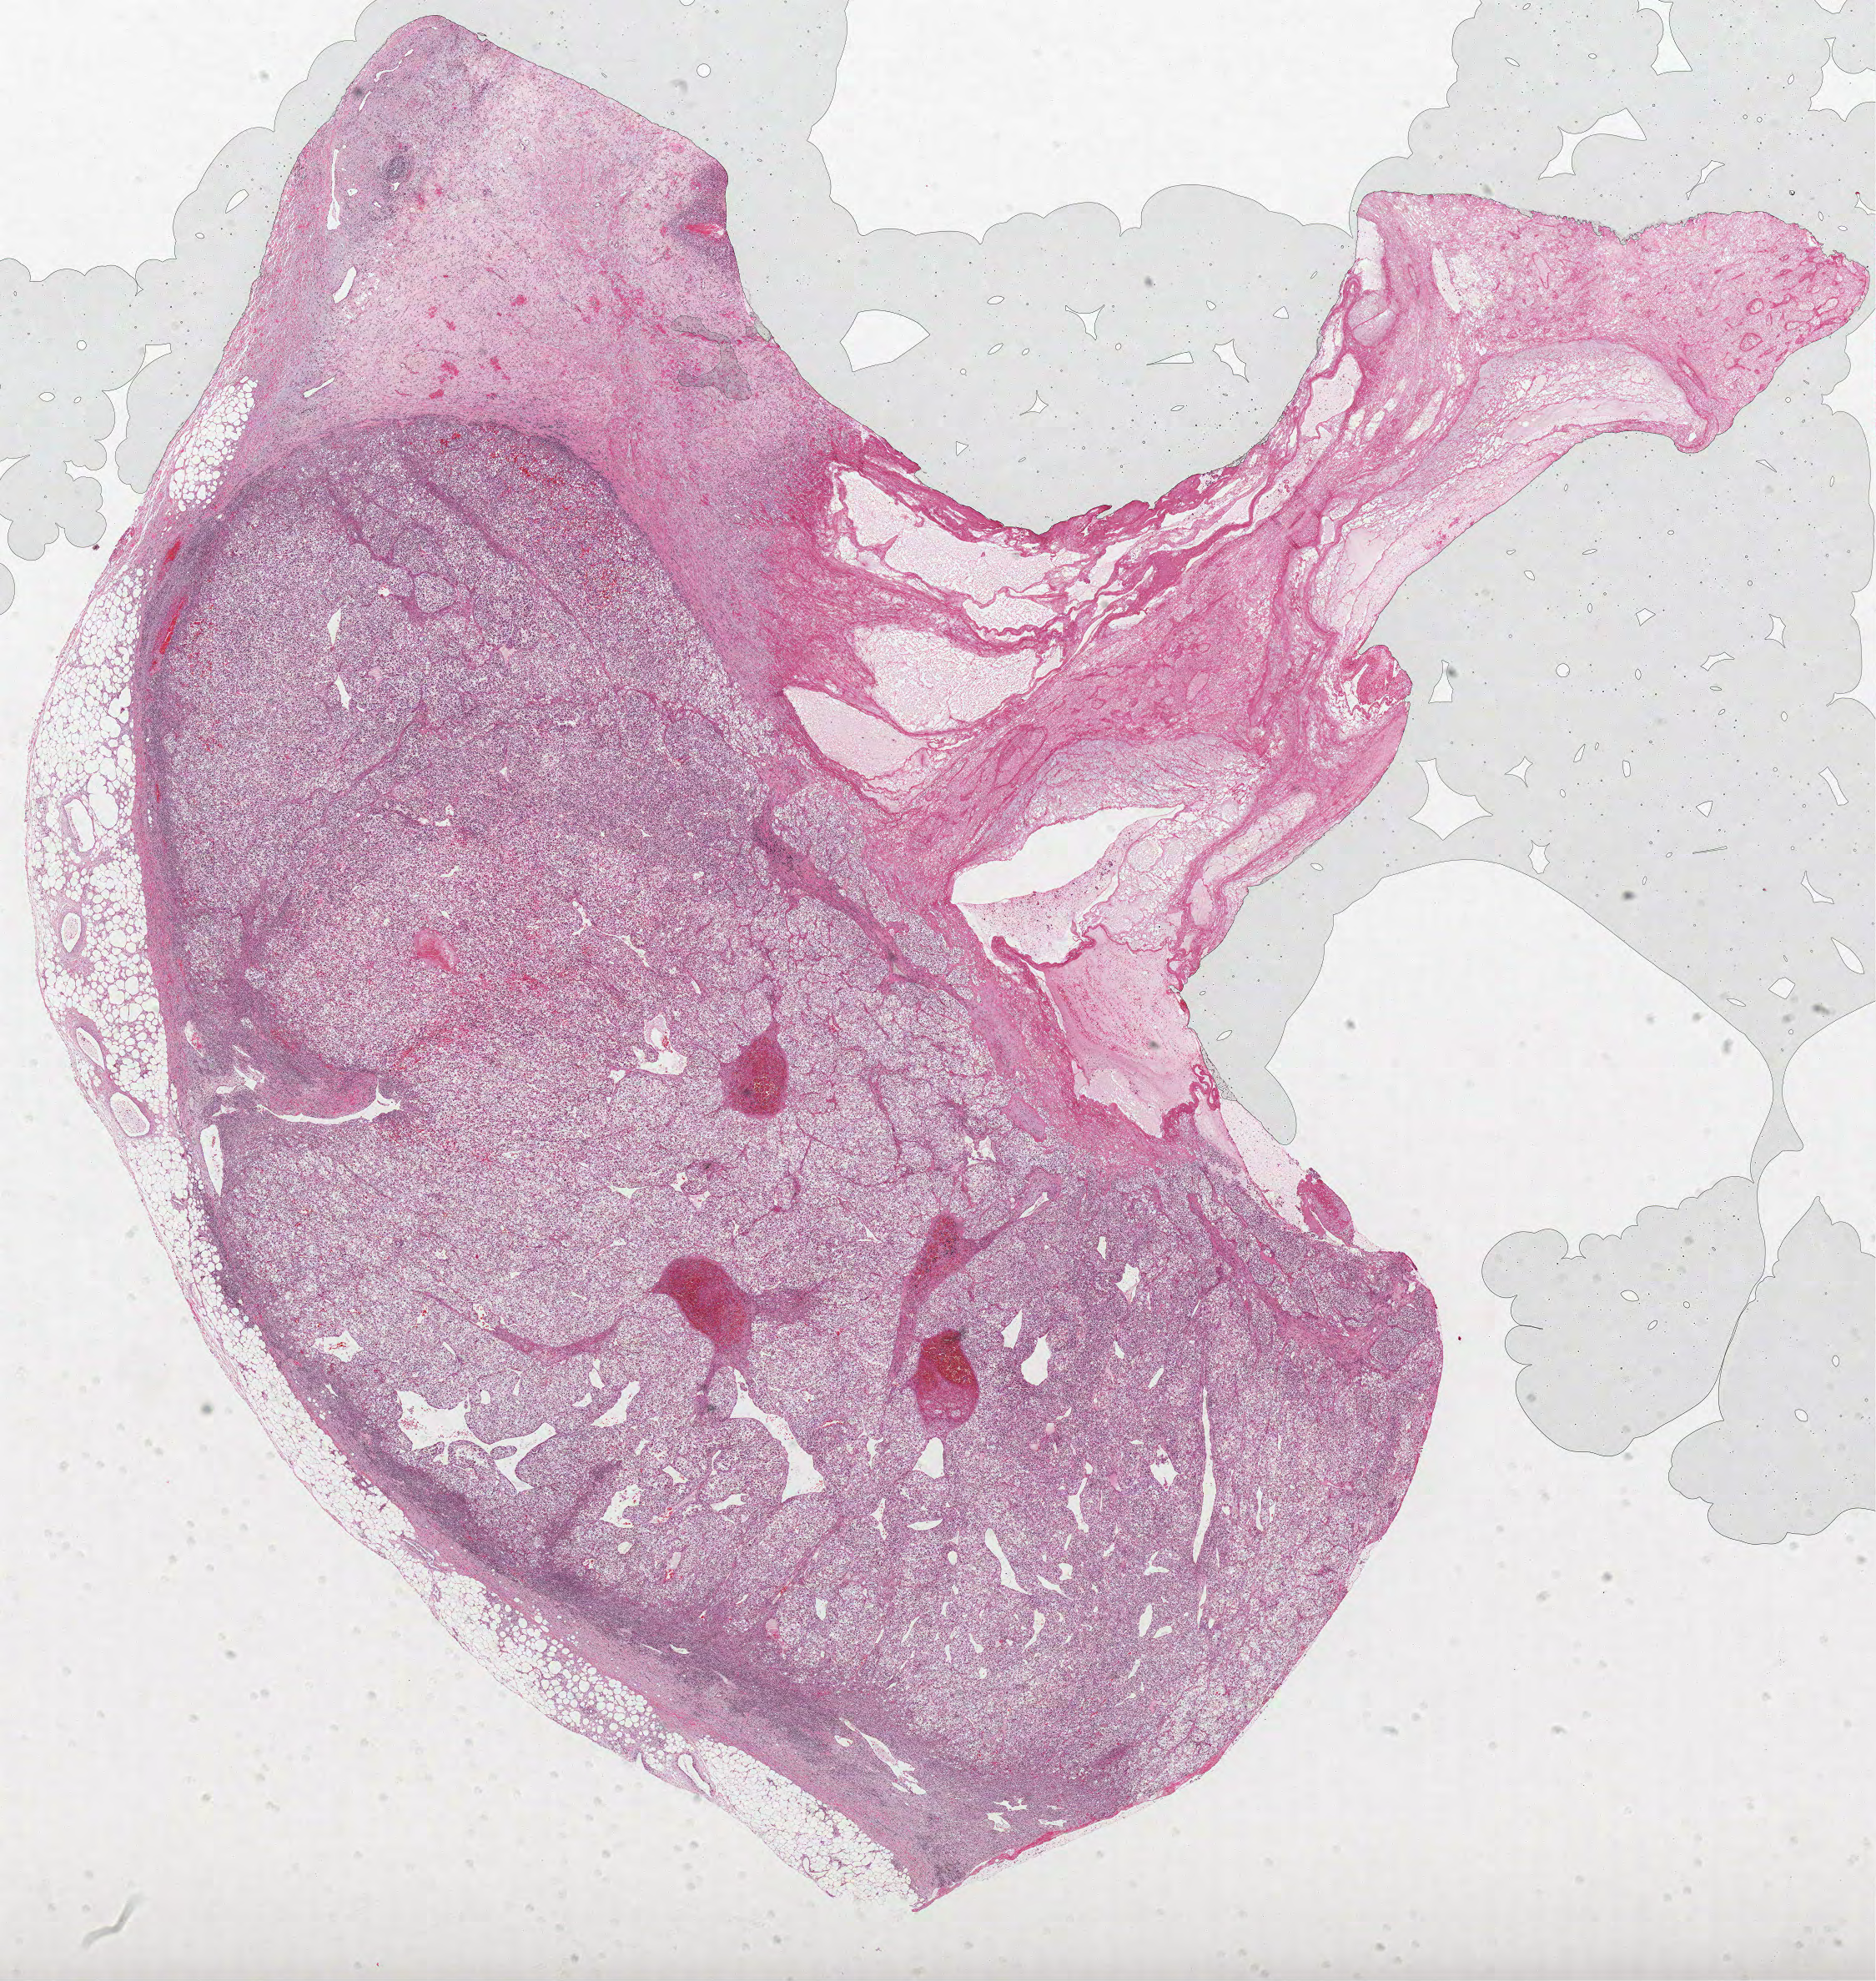
H&E-stained whole-slide image — a low-resolution overview of the entire scanned area, about 18.0 x 19.0 mm (from a 40x scan); formalin-fixed paraffin-embedded (FFPE) diagnostic section; sample: primary tumour, kidney. Female, age 60 years at initial diagnosis. Histologic grade: G3 (poorly differentiated).
Pathologic diagnosis: Clear cell adenocarcinoma, NOS. AJCC pathologic stage: III.